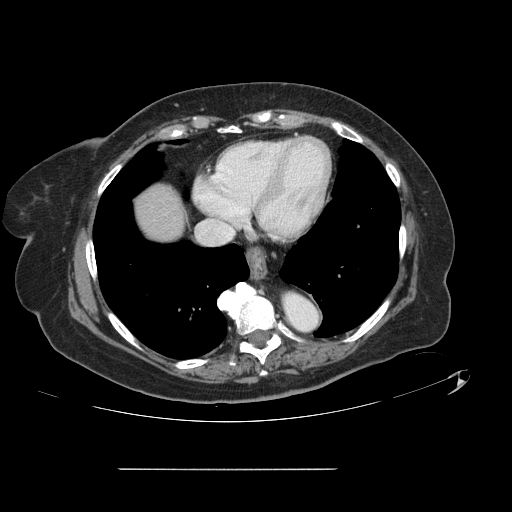
Contrast-enhanced abdominal CT, one axial slice; slice 129 of 148 in the series (ordered by position); 120 kVp; intravenous contrast given; soft-tissue window (W 400 / L 40 HU); 2.5 mm slice thickness; 512 × 512 image matrix. Female patient, age 75 years. Case-level facts recorded for this patient, not image findings: diagnosis: colorectal cancer liver metastases, imaged before liver resection; multiple liver metastases: no; largest metastasis: 2.4 cm; disease in both lobes: no.
Outlined on this slice (expert manual segmentation):
- liver: bounding box [x1, y1, x2, y2] px = [136, 187, 183, 239]
- planned liver remnant (the part of the liver to remain after resection): [136, 187, 183, 240]